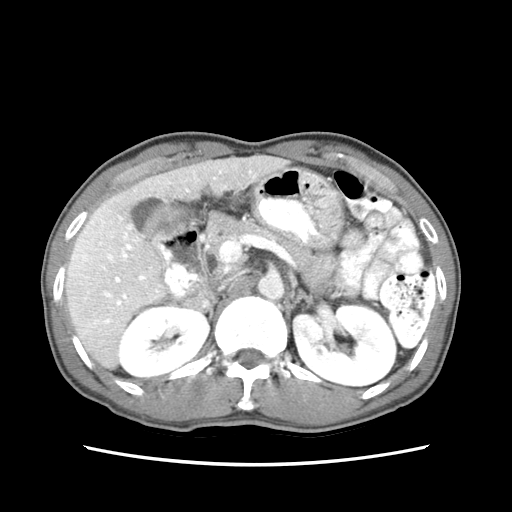
Contrast-enhanced abdominal CT (liver protocol), one axial slice; position 34 of 79 along the scan axis; reconstruction kernel STANDARD; 120 kVp; soft-tissue window (W 400 / L 40 HU); 2.5 mm slice thickness; 512 × 512 image matrix. Case-level facts recorded for this patient, not image findings: diagnosis: hepatocellular carcinoma (patient treated with transarterial chemoembolisation; whether this scan precedes or follows treatment is not stated here); TNM stage (as recorded): Stage-IIIB; Child-Pugh class: A; tumour differentiation: moderately differentiated; tumour nodularity: multinodular.
Structures marked on this image (semi-automatically segmented with operator editing):
- liver parenchyma outside the tumour (the mass and vessels are separate outlines, so this box may not span the whole liver): bounding box [x1, y1, x2, y2] px = [64, 152, 287, 368]
- liver vessels: [71, 162, 267, 340]